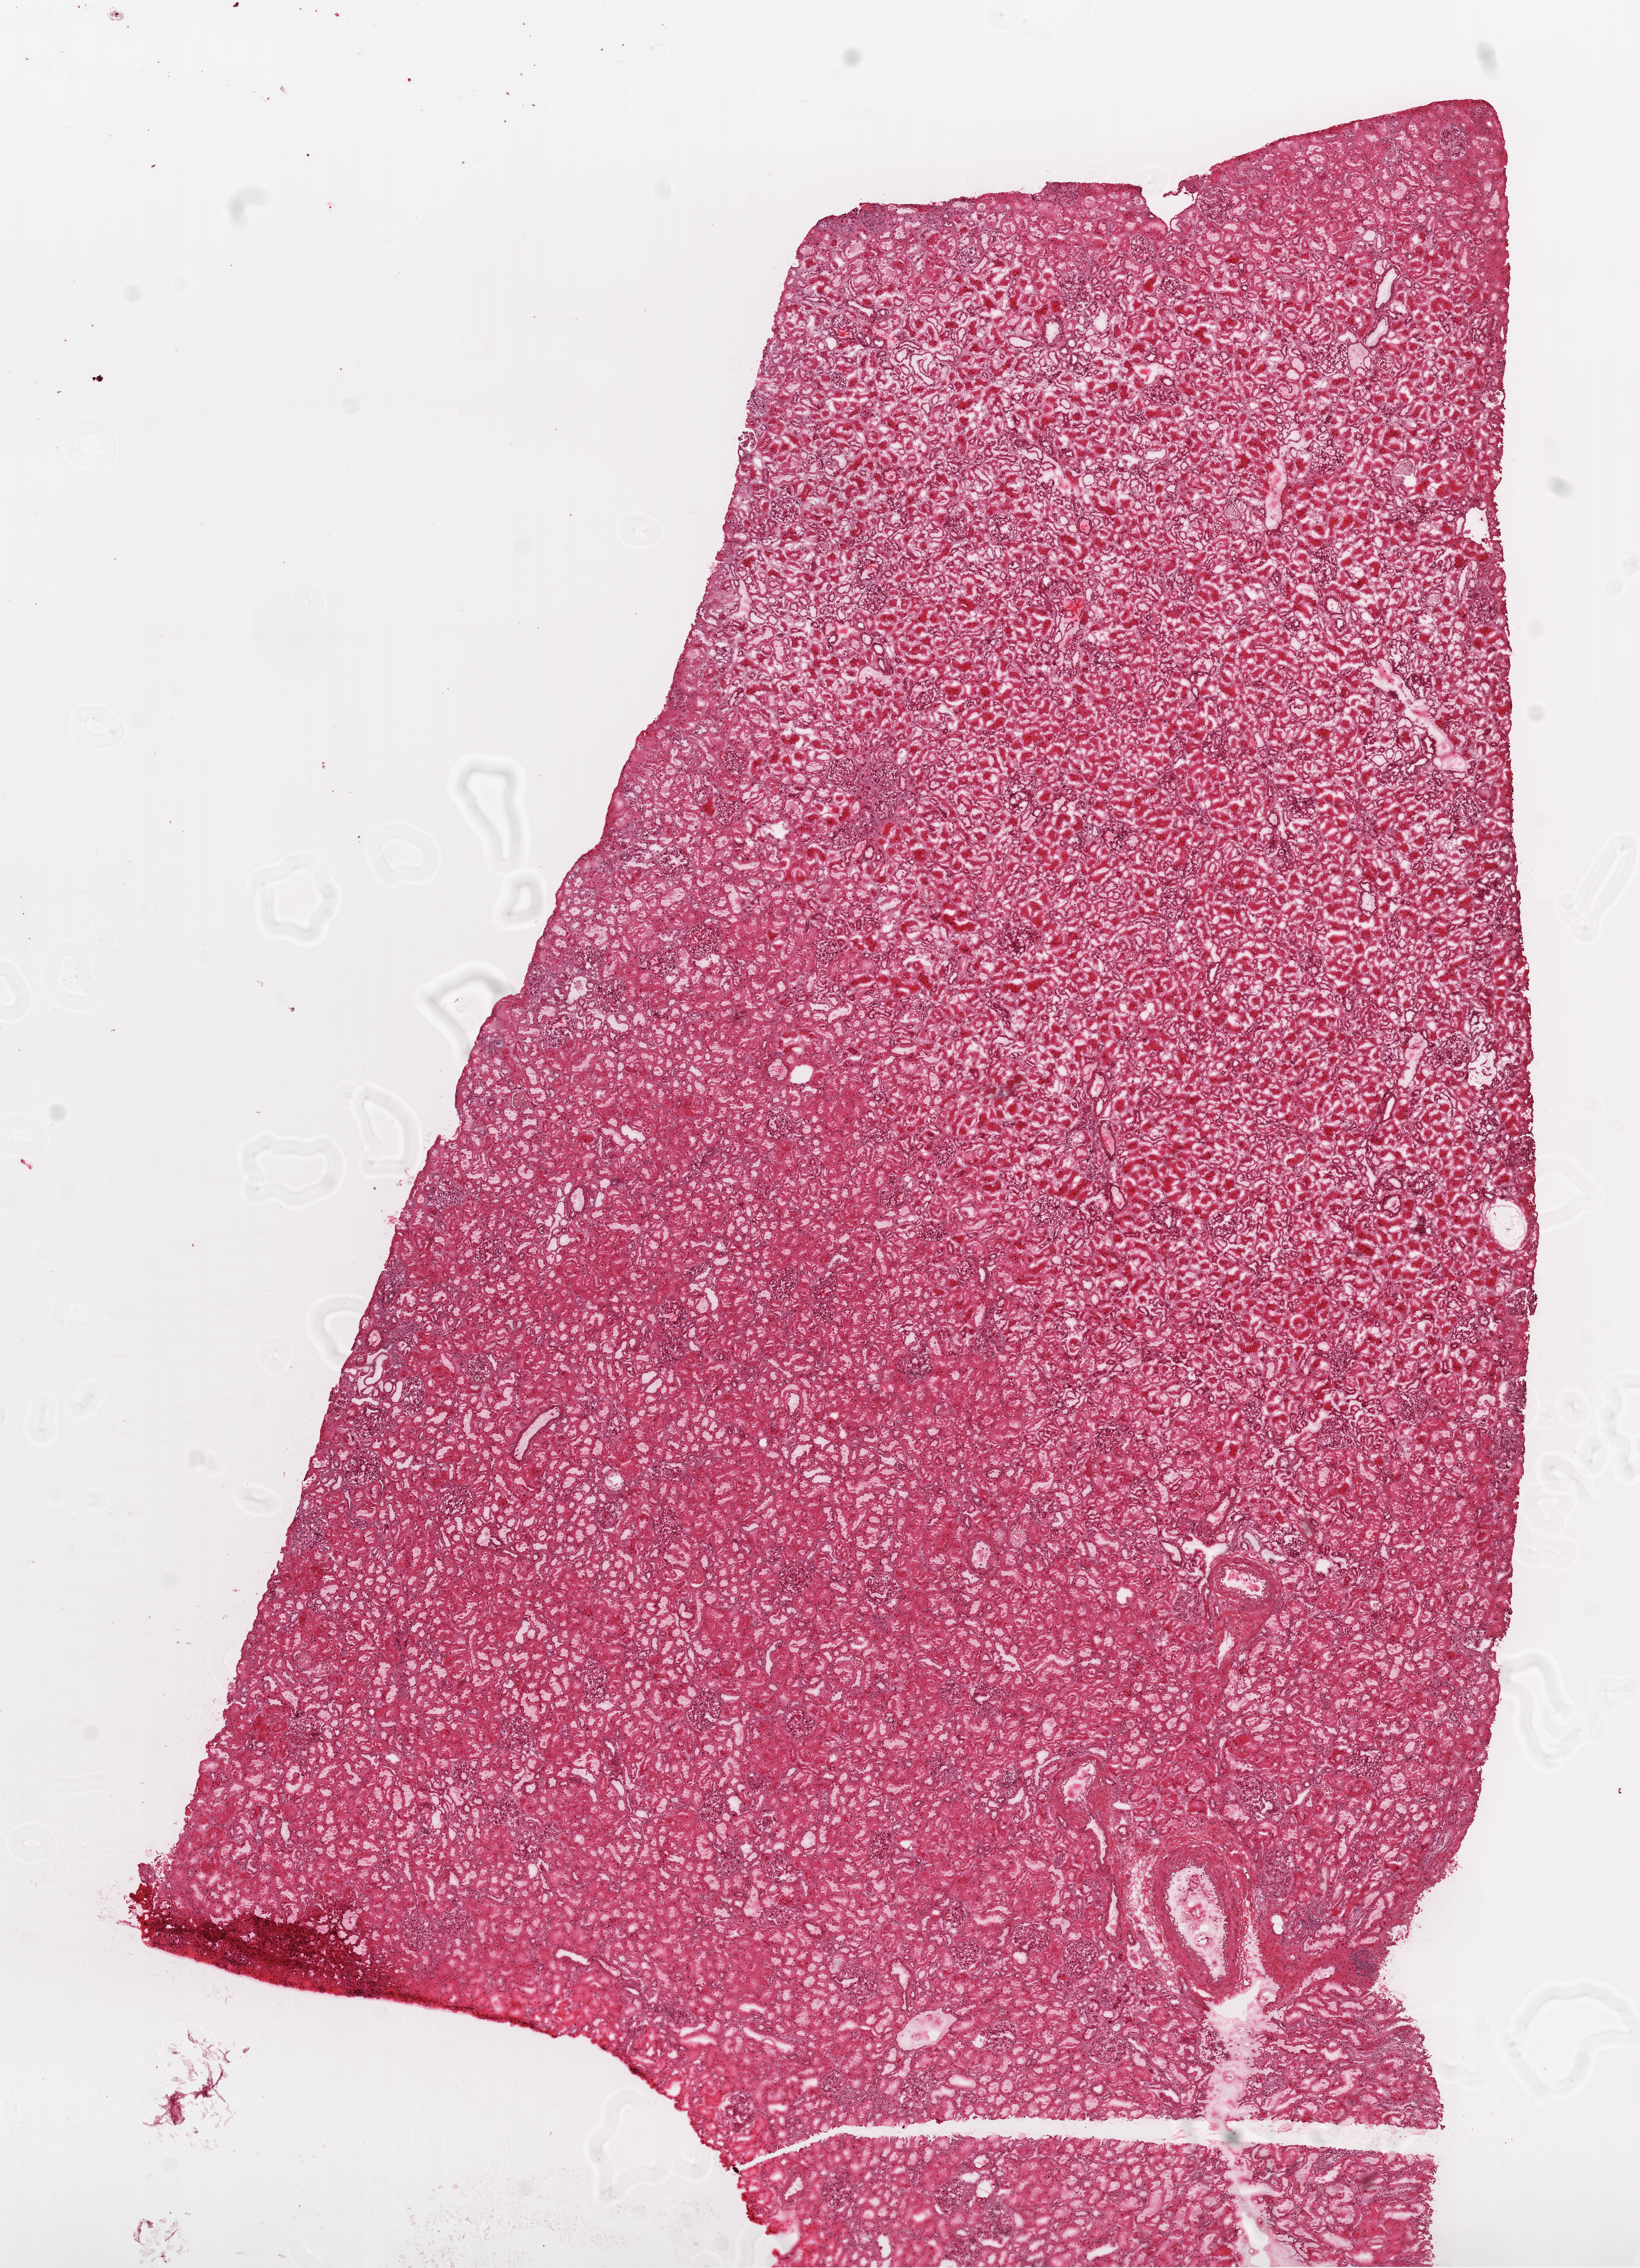
H&E whole-slide image, a low-resolution overview of the entire scanned area, about 9.0 x 12.5 mm, frozen section from the top of the tissue portion, kidney, solid tissue normal (non-tumour tissue) sample. Male, age 47 years at initial diagnosis.
This section: solid tissue normal (non-tumour) sample from the same patient. Patient diagnosis: Clear cell adenocarcinoma, NOS.